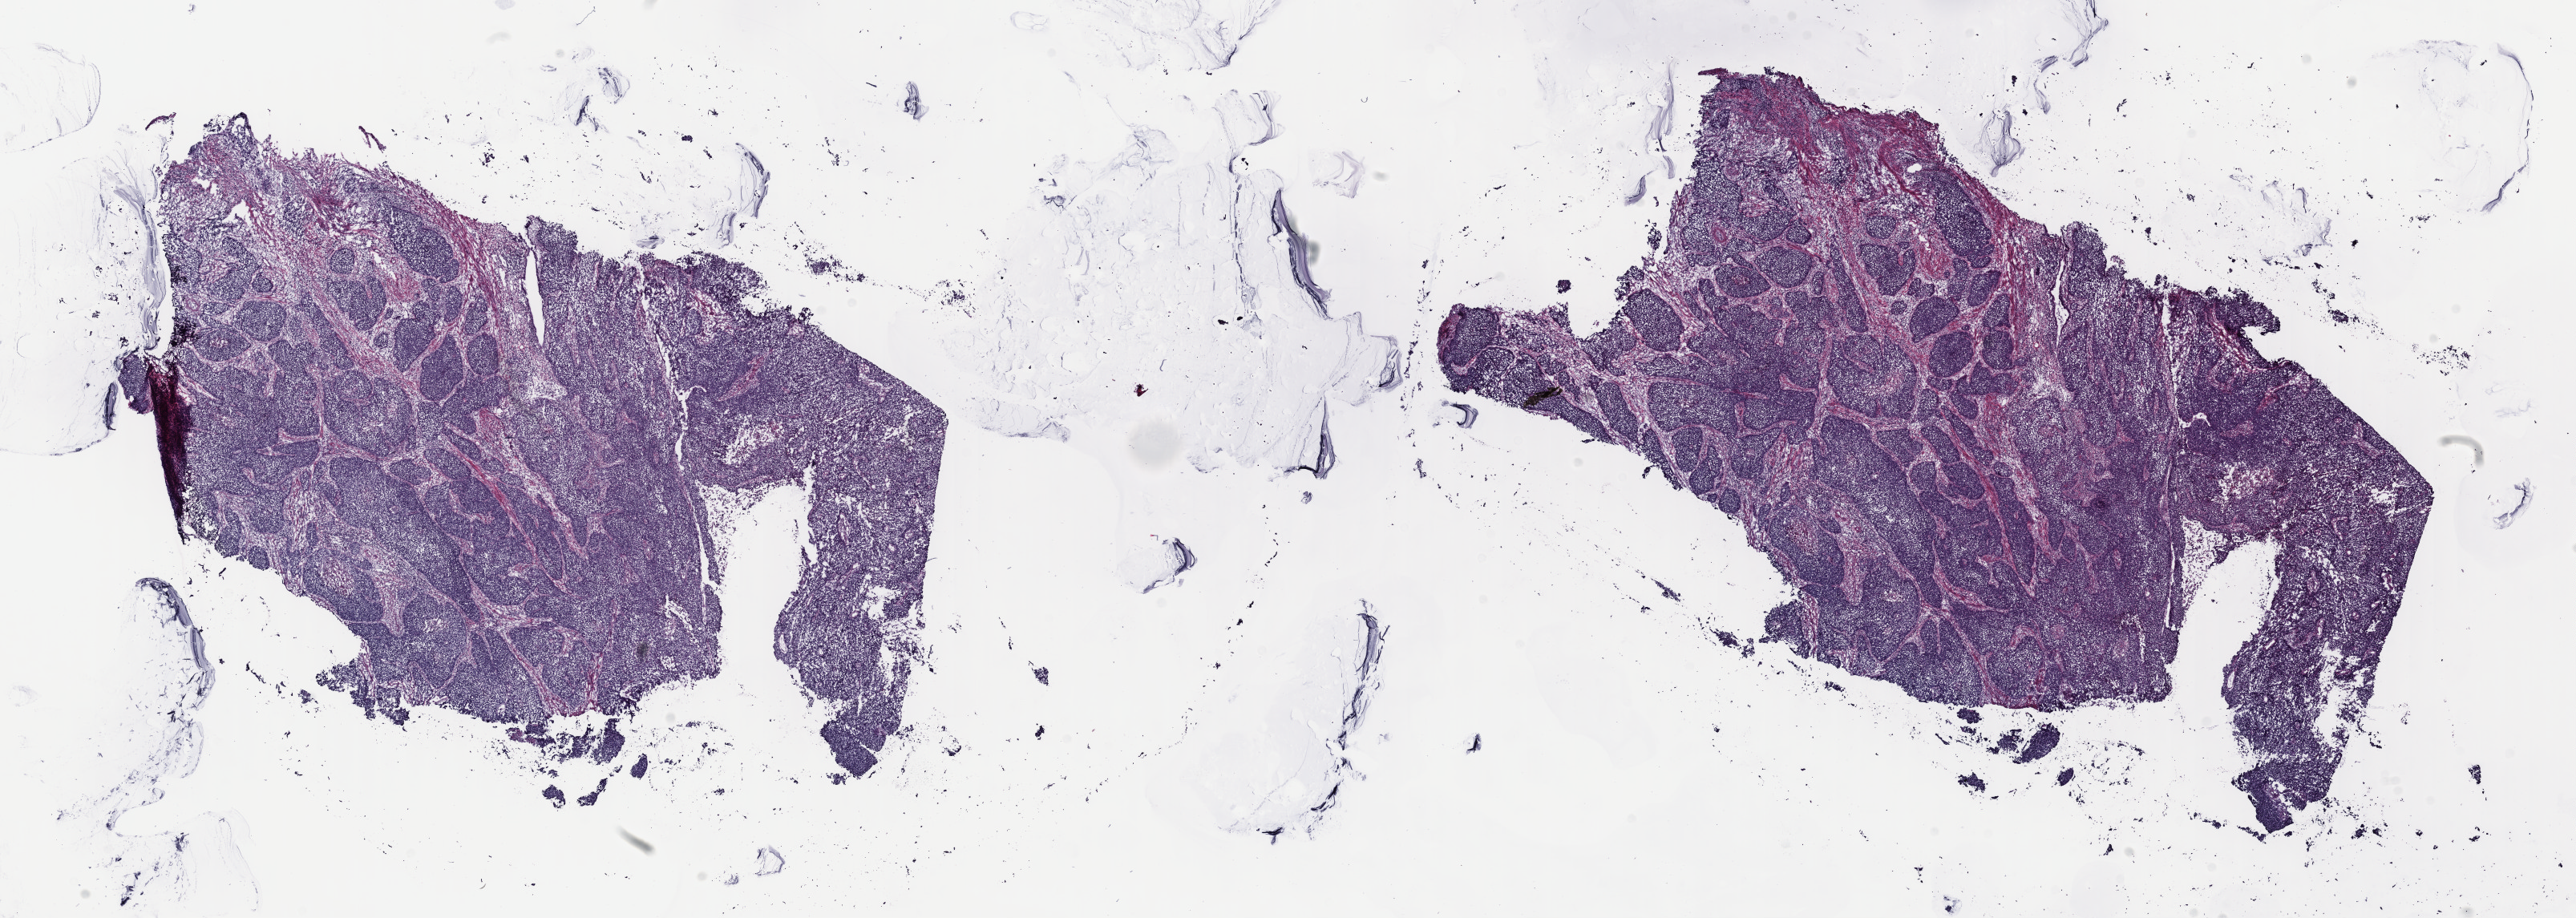
Digitized H&E-stained tissue section (whole slide), a low-resolution overview of the entire scanned area, about 25.3 x 9.0 mm (from a 40x scan). Frozen section from the top of the tissue portion. Primary tumour sample from the cervix. Female, age 47 years at initial diagnosis. Histologic grade: G2 (moderately differentiated). Pathologist review of this section (percent, as recorded): tumour cells 70%, tumour nuclei 70%, normal cells 0%, stromal cells 25%, necrosis 5%. Infiltration values recorded for this section: lymphocyte infiltration 60%, monocyte infiltration 10%, neutrophil infiltration 20%.
FIGO stage: IB. Diagnosis: Squamous cell carcinoma, large cell, nonkeratinizing, NOS. Lymph nodes positive (case pathology): 0 of 18 examined.